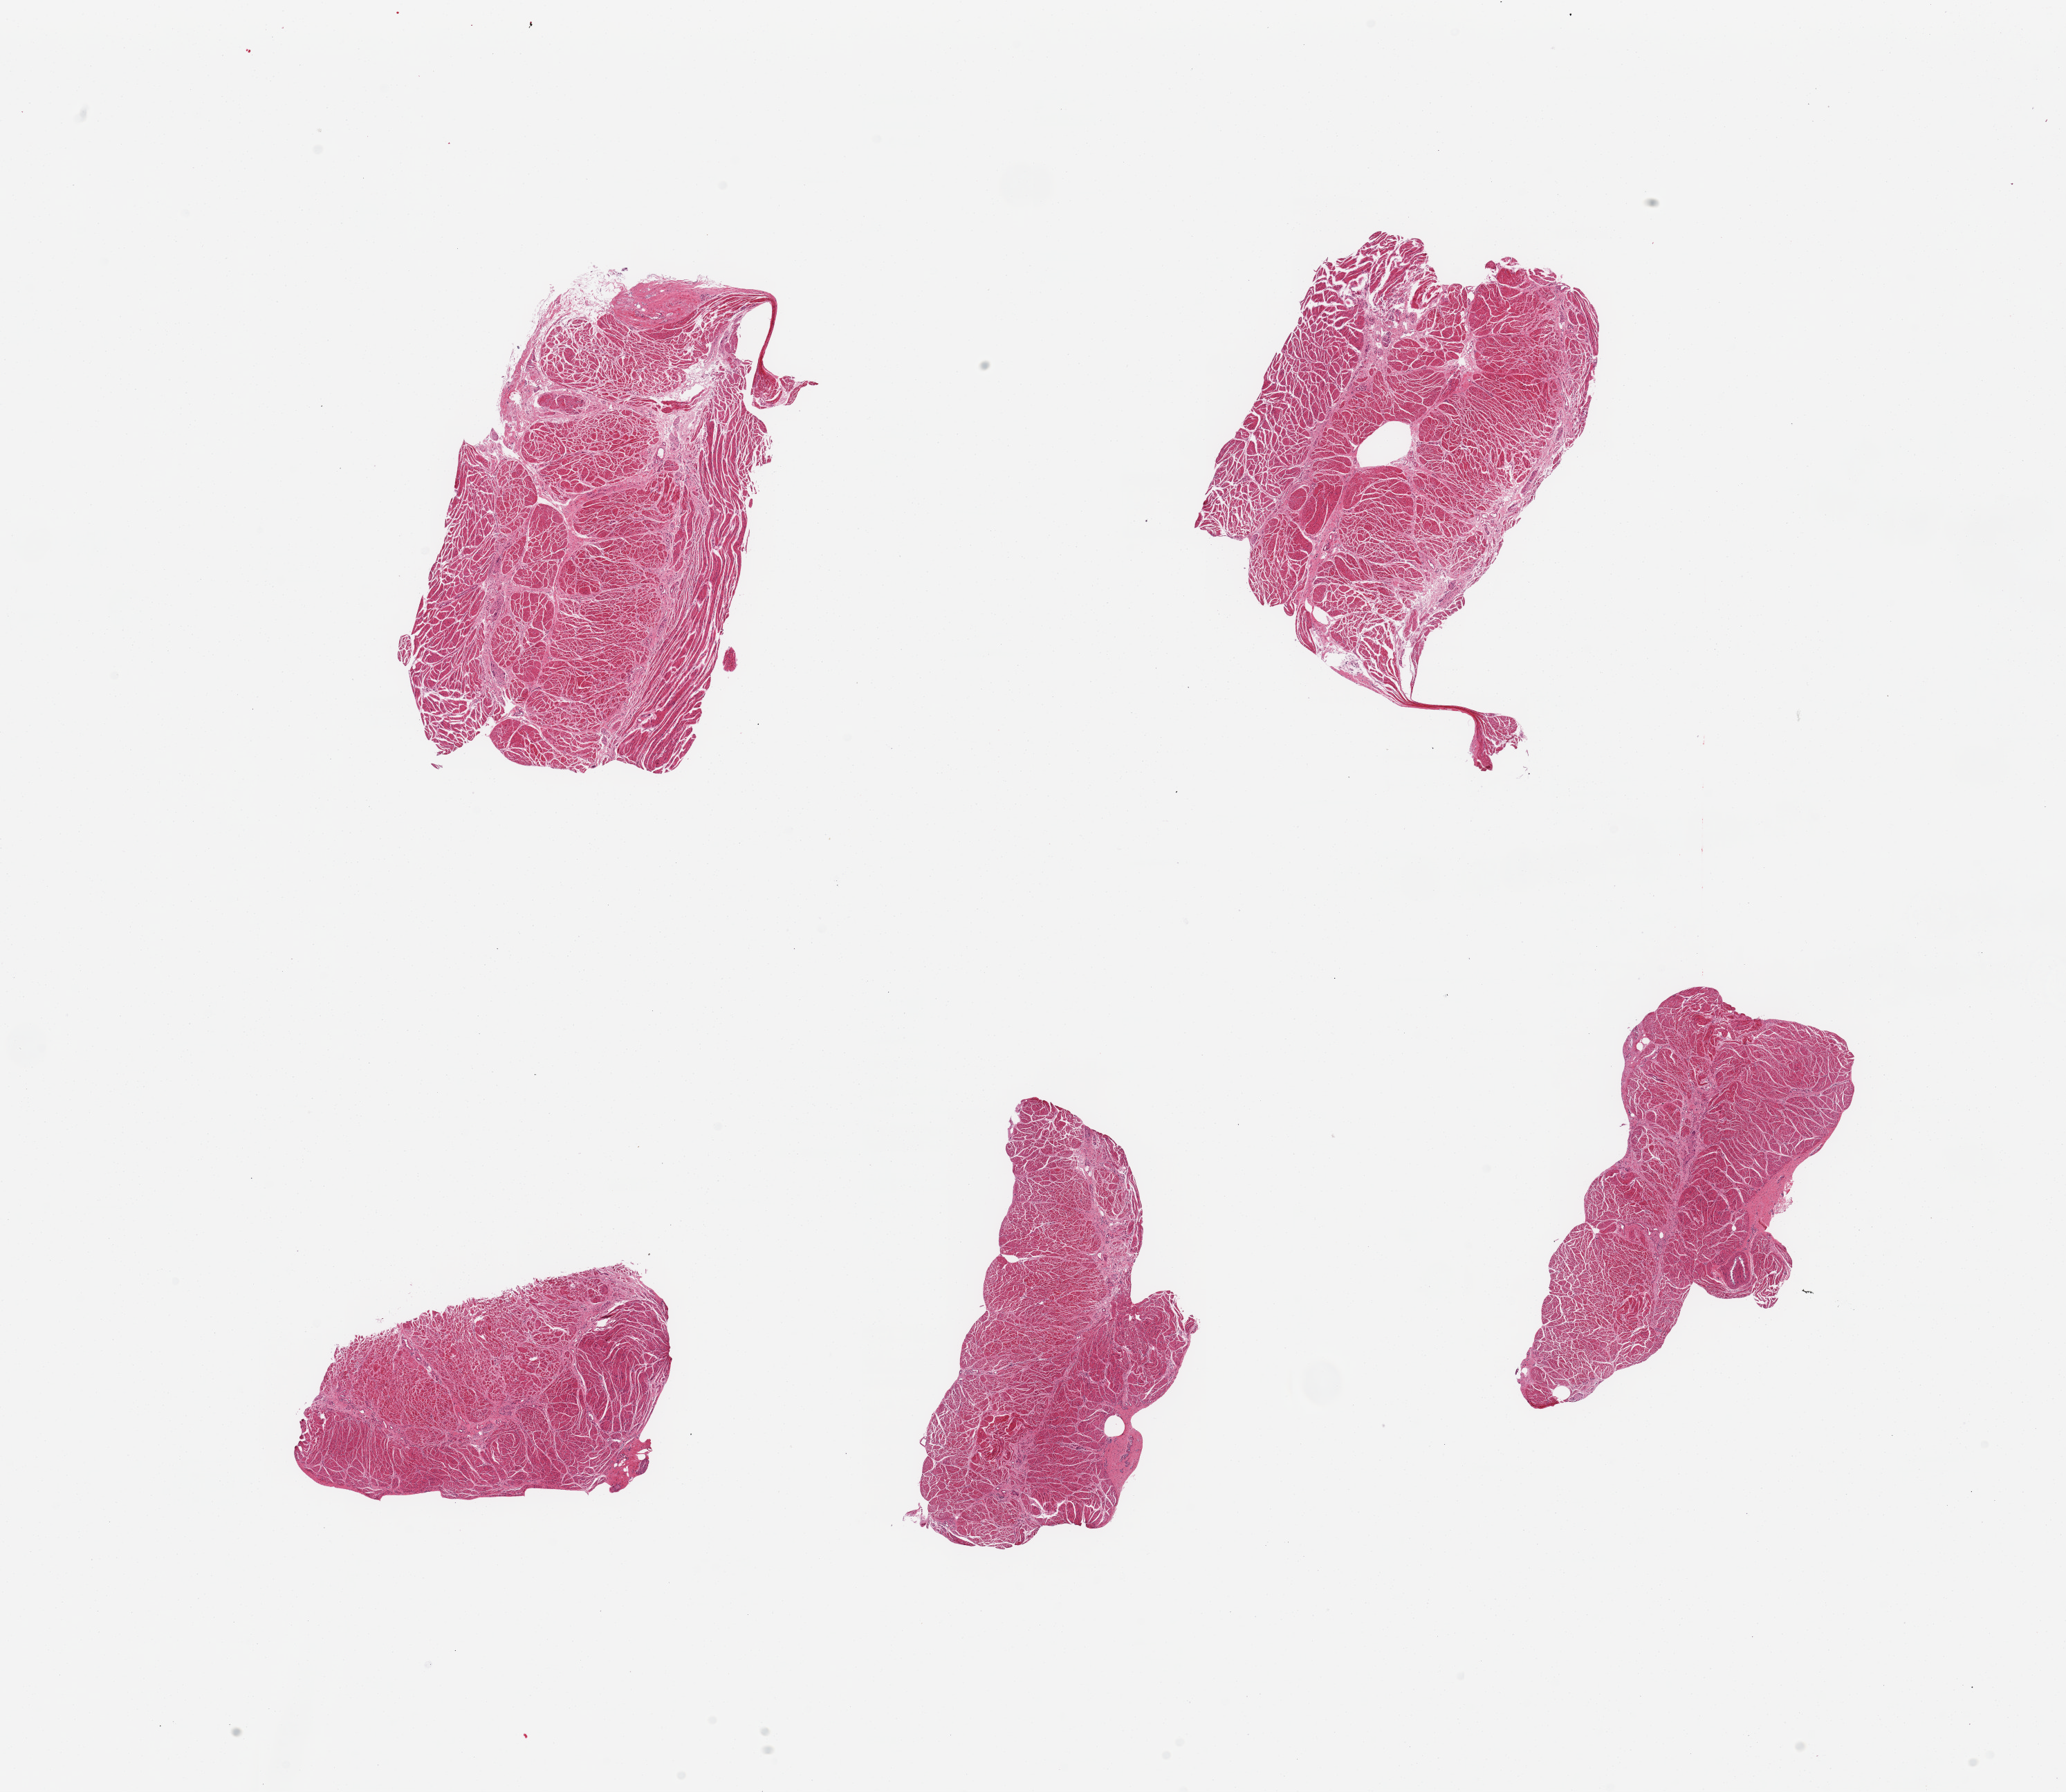
H&E whole-slide image, a low-resolution overview of the entire scanned area, about 23.6 x 20.5 mm, PAXgene-fixed, paraffin-embedded tissue, target tissue: gastroesophageal junction, donor tissue sample. Female donor.
- review note (as recorded): 5 pieces; well trimmed target muscularis